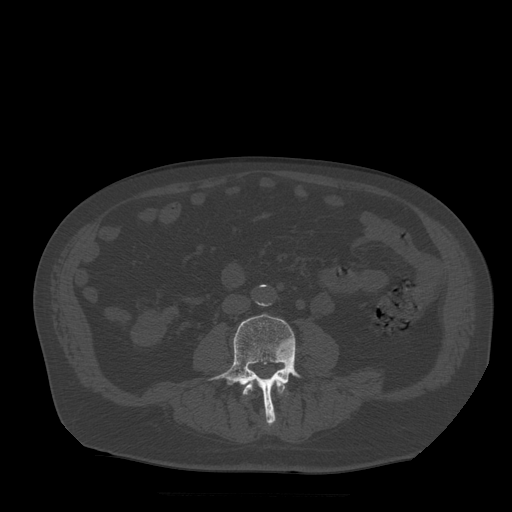
CT including the spine, one axial slice; position 117 of 522 along the scan axis; bone window (W 1800 / L 400 HU); 512 × 512 image matrix, field of view 420 × 420 mm. Patient age 72 years. Case-level facts recorded for this patient, not image findings: primary cancer: prostate.
Structures marked on this image (semi-automatically segmented with operator editing):
- L3 vertebra: bounding box (x1, y1, x2, y2) in pixels: (243, 379, 289, 396)
- L4 vertebra: (206, 314, 302, 424)